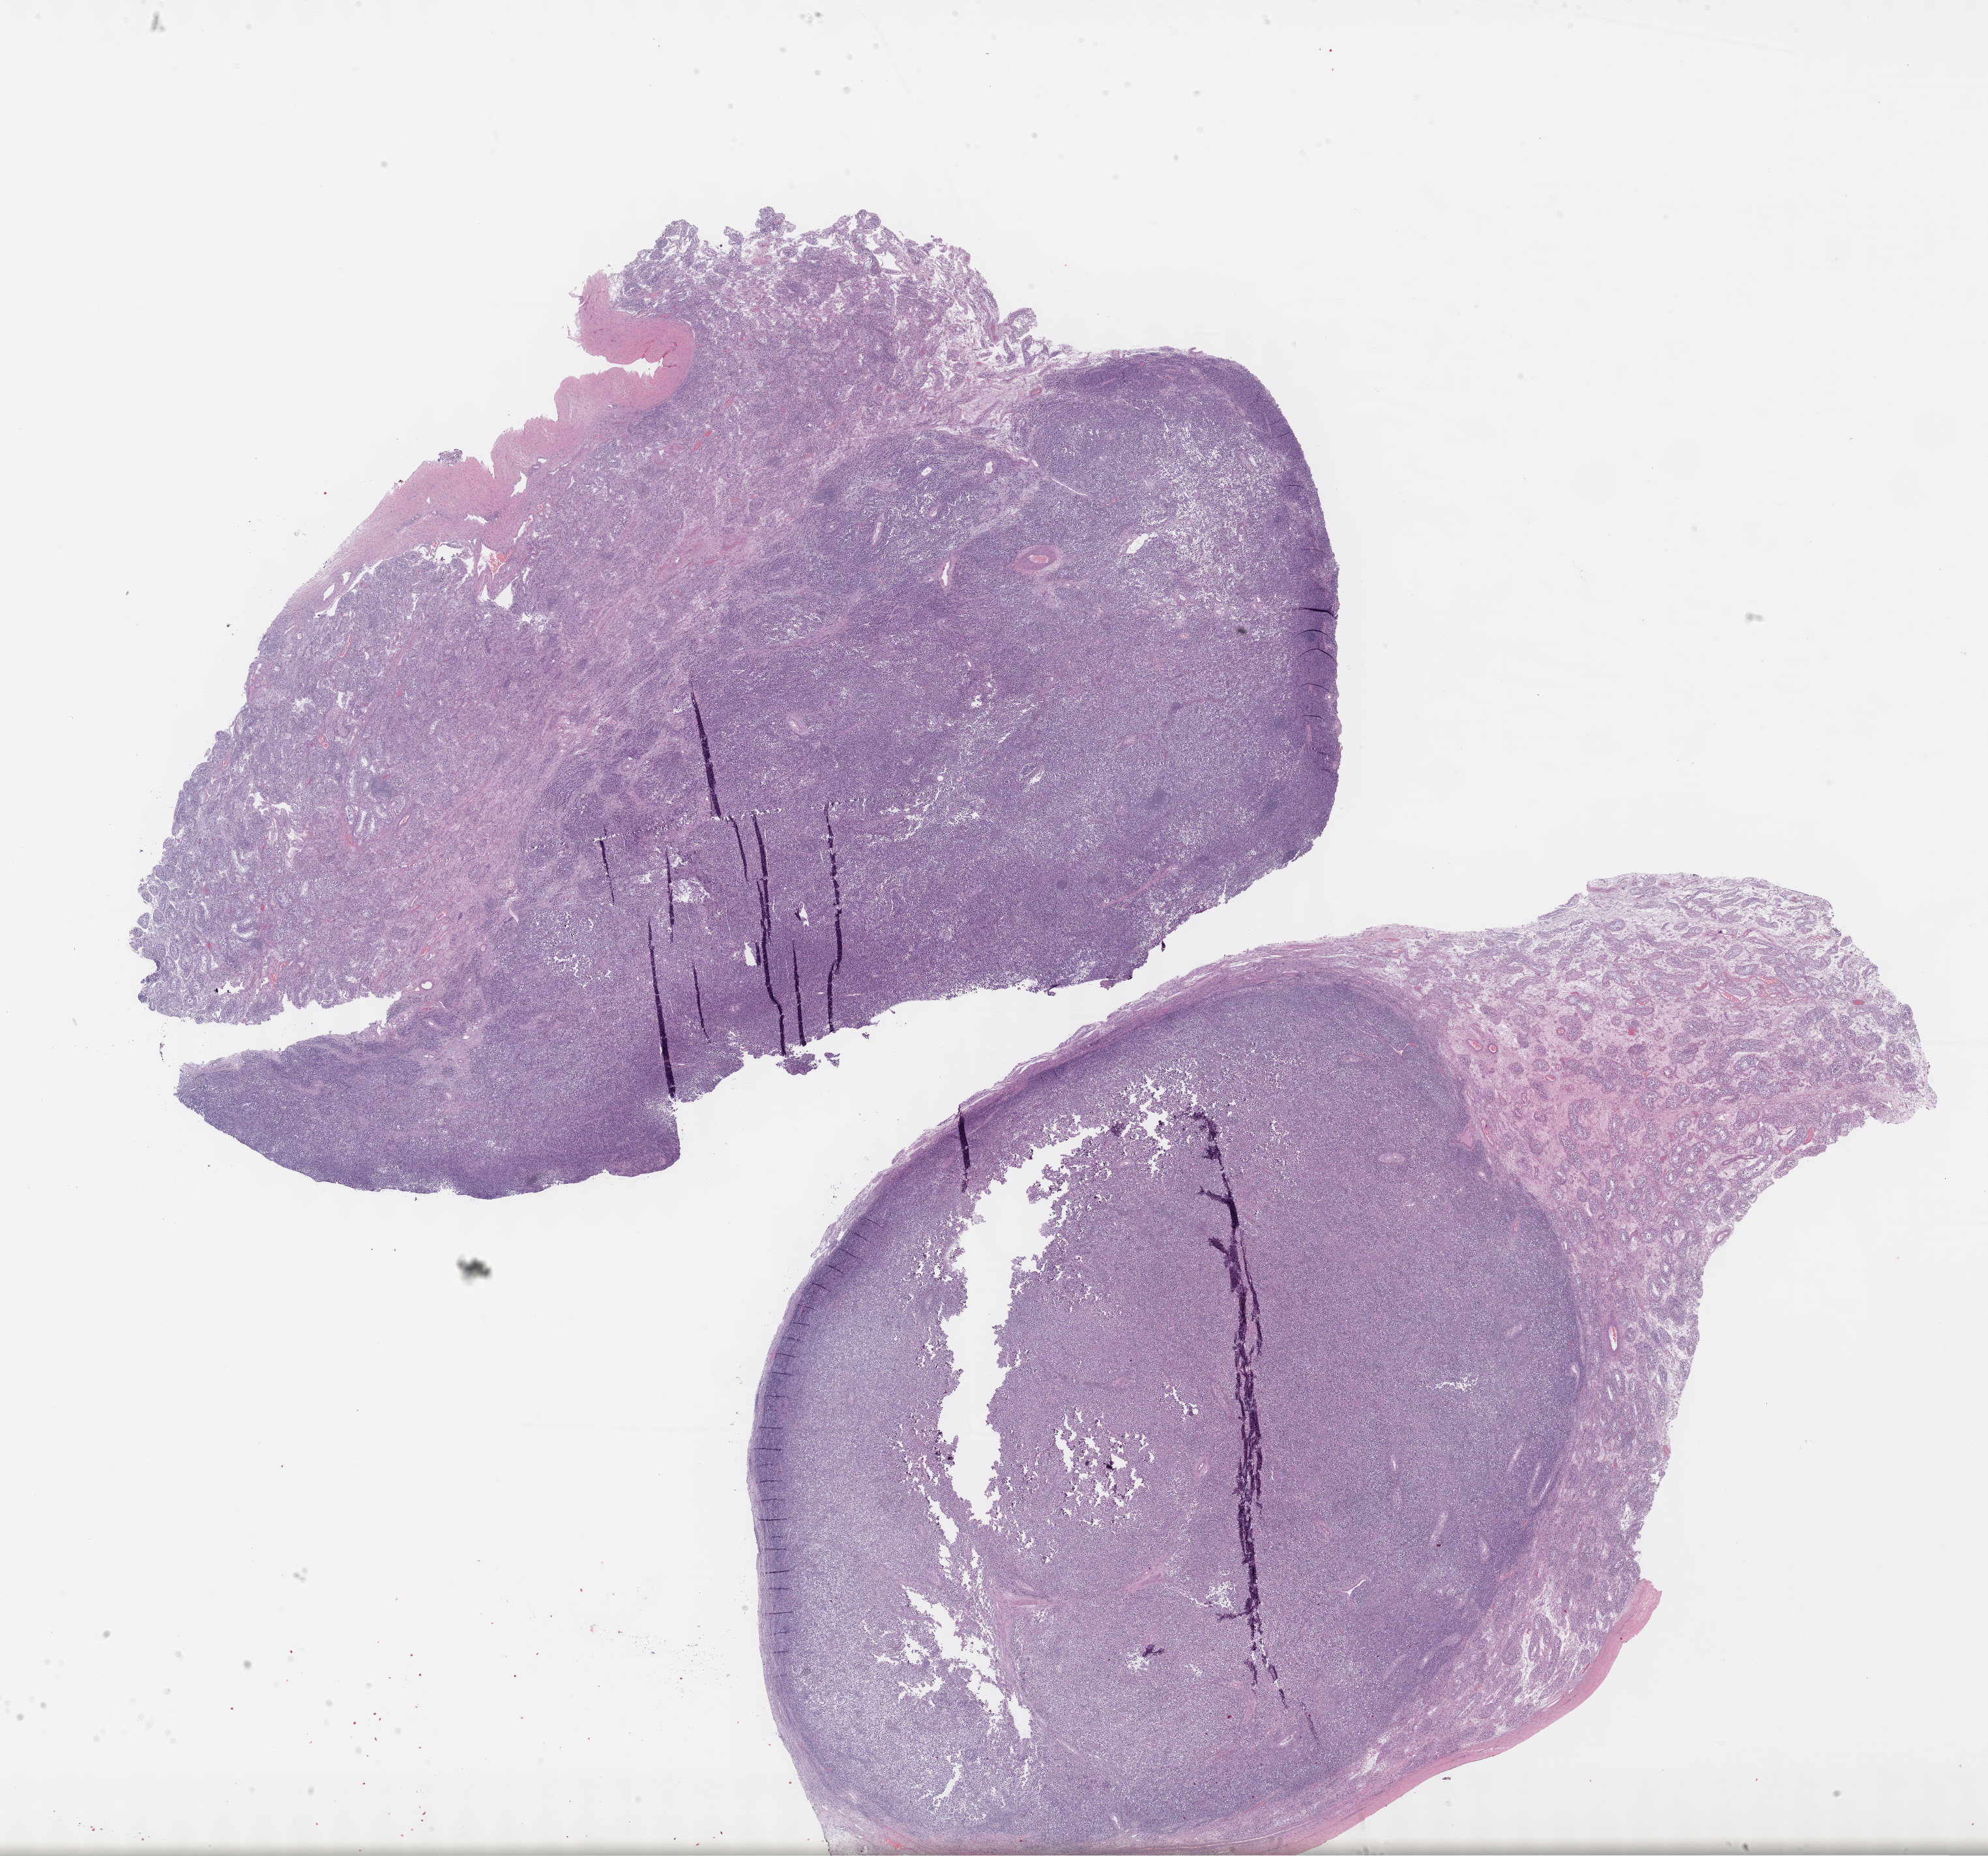
Whole-slide histology image, Hematoxylin and eosin (H&E) stained, whole scanned area (about 24.7 x 23.0 mm) shown as a low-resolution overview. Formalin-fixed paraffin-embedded (FFPE) diagnostic section. Primary tumour sample from the testis. Male, age 22 years at initial diagnosis.
Pathologic diagnosis: Seminoma, NOS. Laterality: right. AJCC pathologic stage: IA (7th edition). TNM: T1 NX M0.